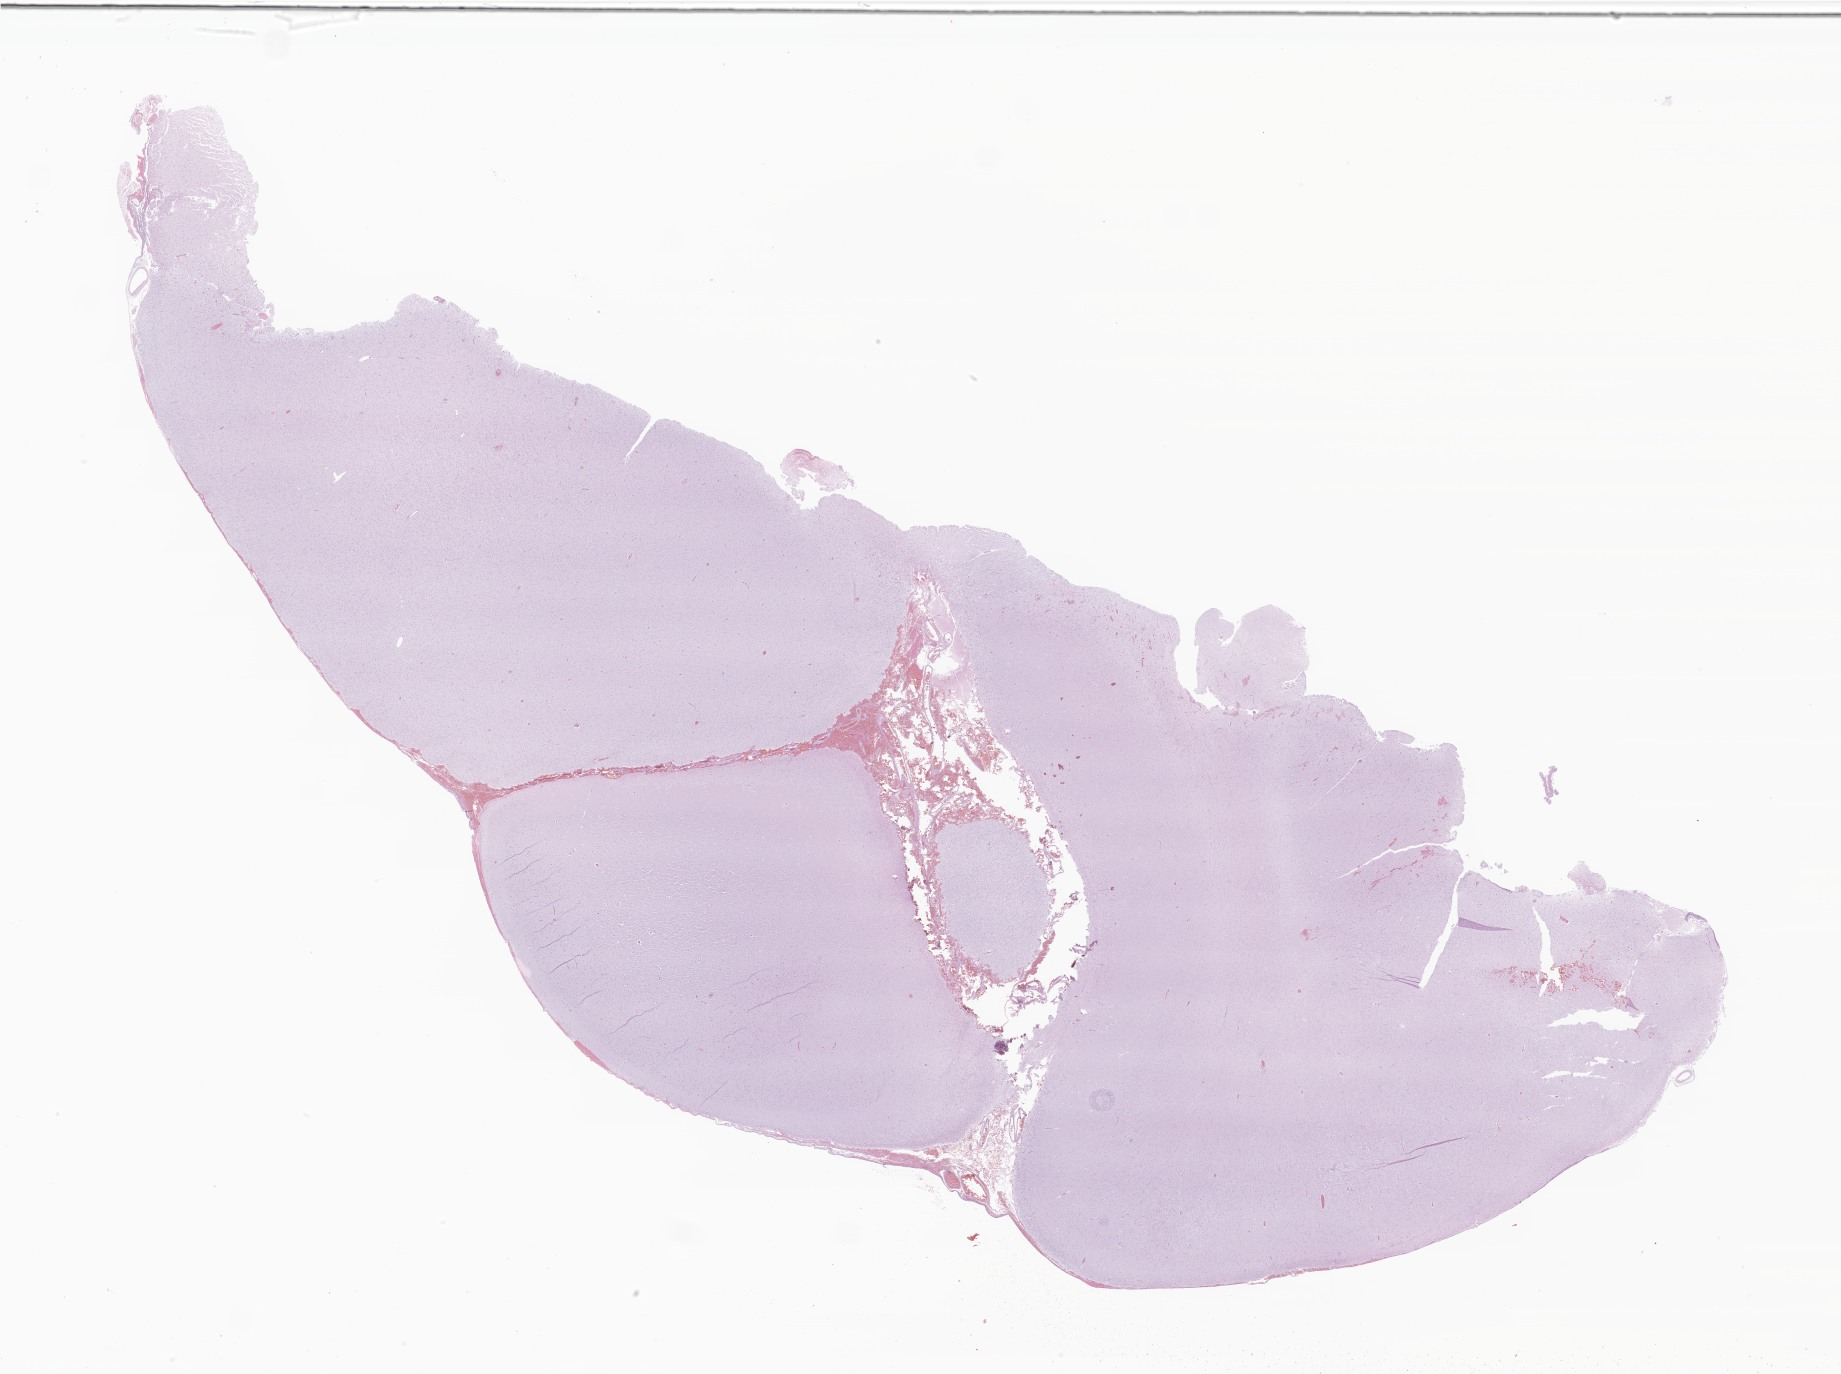
Digitized hematoxylin and eosin (H&E)-stained section of tumor tissue from the temporal lobe, whole scanned area (about 31.1 x 23.2 mm) shown as a low-resolution overview. FFPE section. Patient: female, age 677 days (about 1.9 years).
* diagnosis: Ganglioglioma, NOS